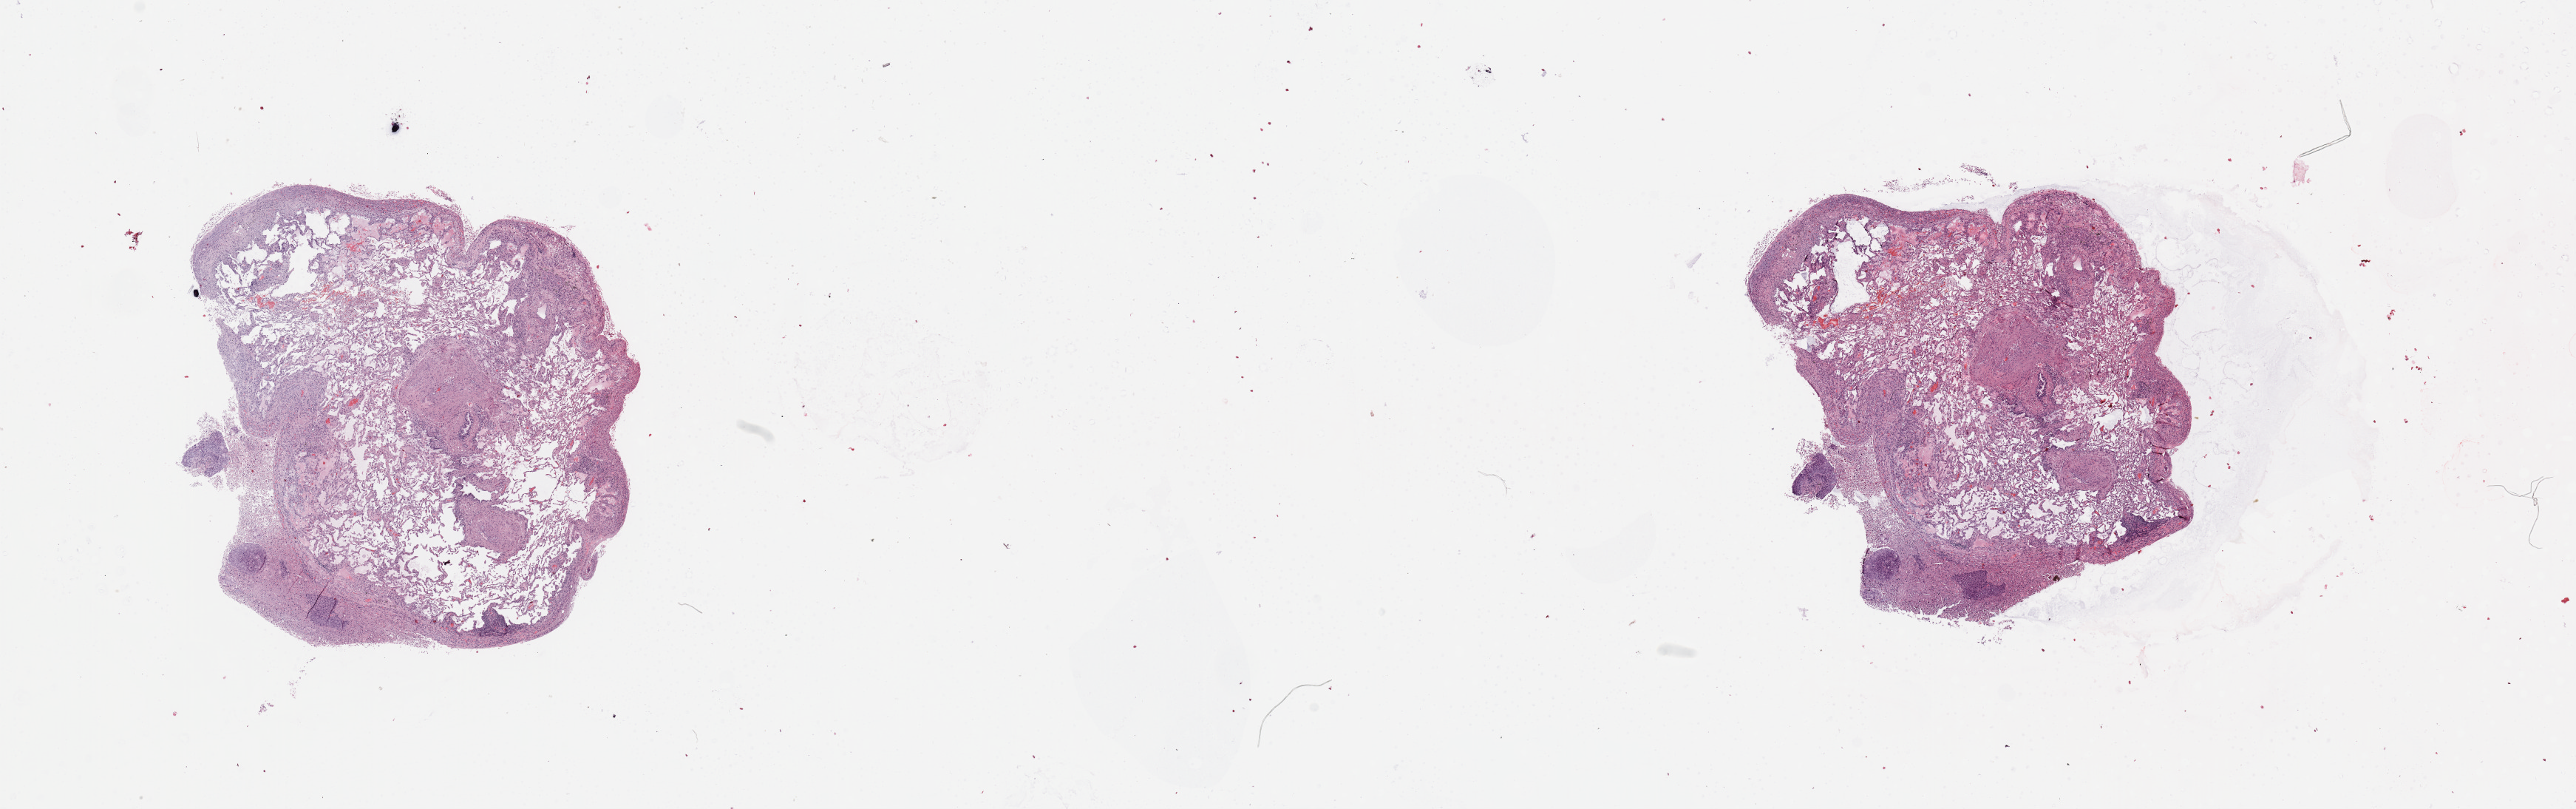
Hematoxylin and eosin (H&E) stained whole-slide image — low-resolution overview of the scanned area, about 27.6 x 8.7 mm (slide scanned at 20x). Lung, normal (non-tumour) tissue. Patient: male, age 70 years.
* this section: normal (non-tumour) tissue from the same patient
* patient diagnosis: Squamous cell carcinoma, NOS